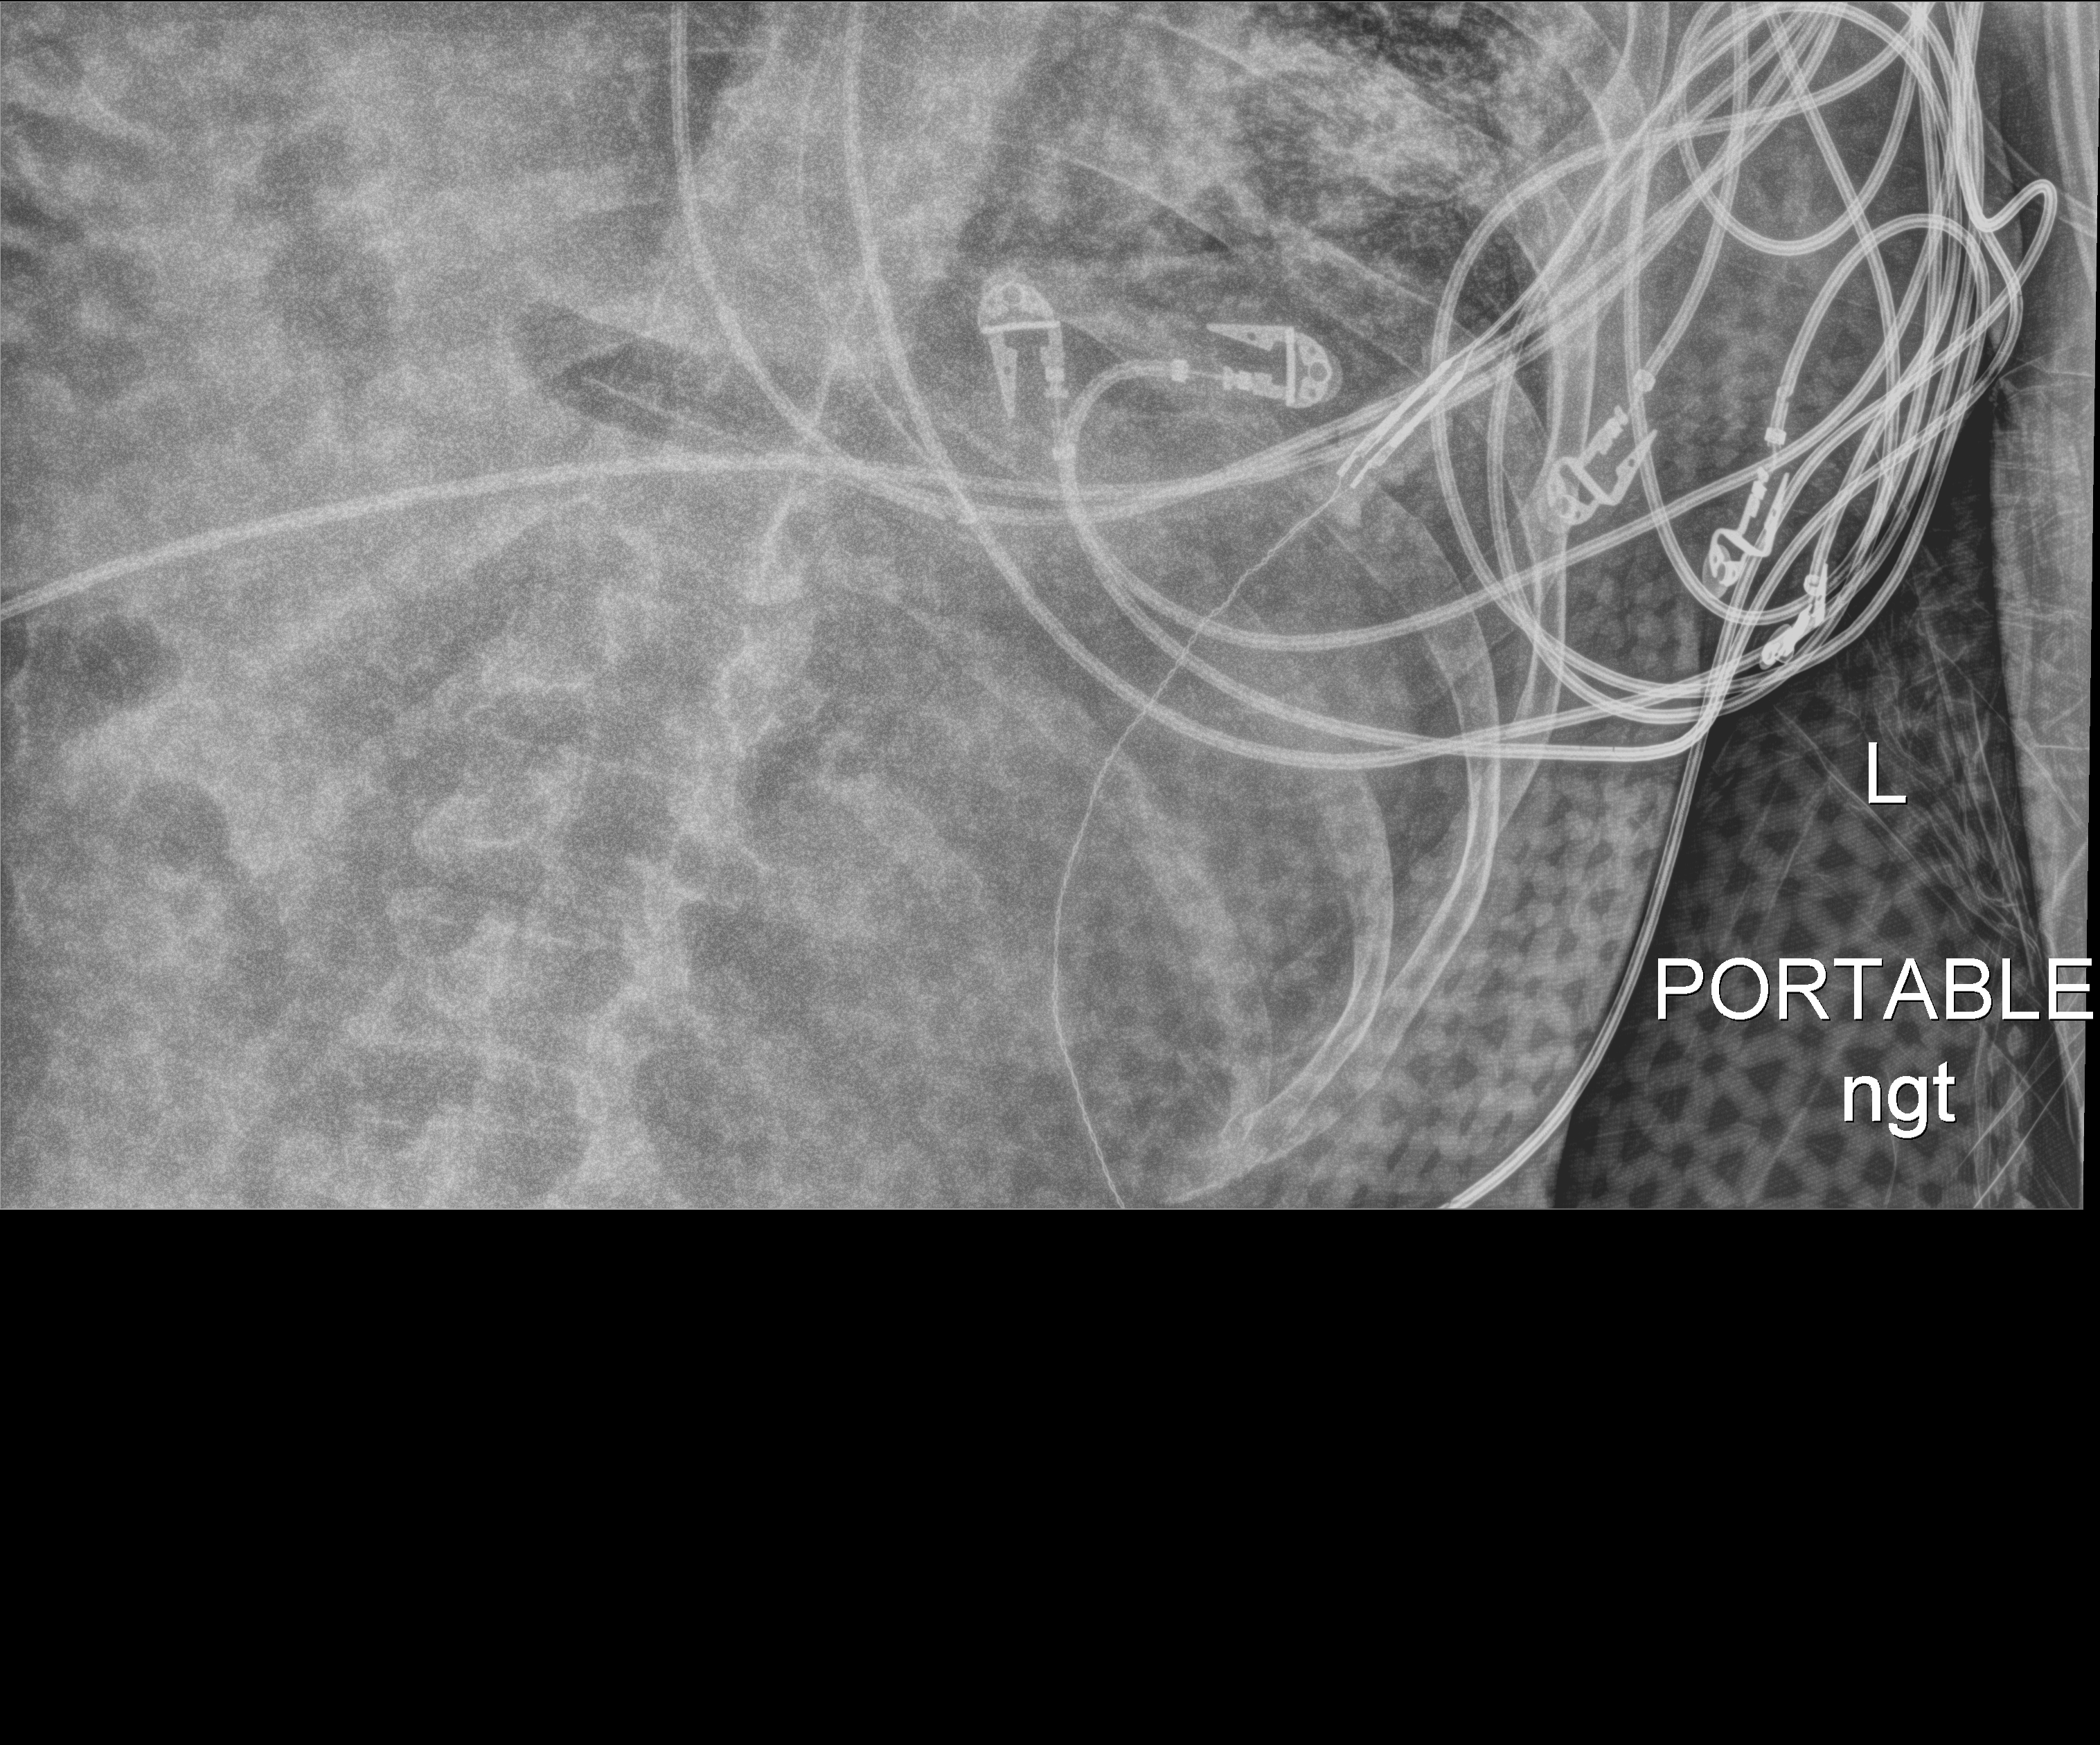
Chest X-ray (portable), anteroposterior (AP) projection. Patient hospitalised with COVID-19; male, aged 18–59 years.
Hospital-stay facts (about this admission, not read from this image; timing relative to this image not recorded): other chronic lung disease (admission record): no; diabetes (admission record): no.